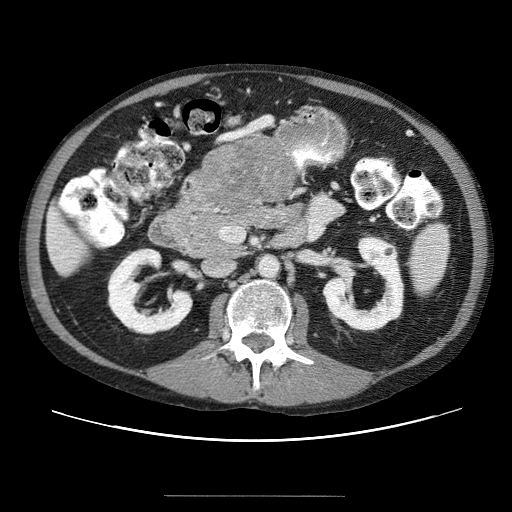
Contrast-enhanced abdominal CT (liver protocol), one axial slice; reconstruction kernel STANDARD; soft-tissue window (W 400 / L 40 HU); 512 × 512 image matrix, field of view 380 × 380 mm. Case-level facts recorded for this patient, not image findings: diagnosis: hepatocellular carcinoma (patient treated with transarterial chemoembolisation; whether this scan precedes or follows treatment is not stated here); TNM stage (as recorded): Stage-IVB.
Annotated regions visible in this slice (semi-automatic segmentation, software-assisted and operator-edited):
- liver parenchyma outside the tumour (the mass and vessels are separate outlines, so this box may not span the whole liver): box from (x=46, y=145) to (x=238, y=274) px
- mass: (x=185, y=146)–(x=296, y=210)
- liver vessels: (x=61, y=245)–(x=64, y=247)